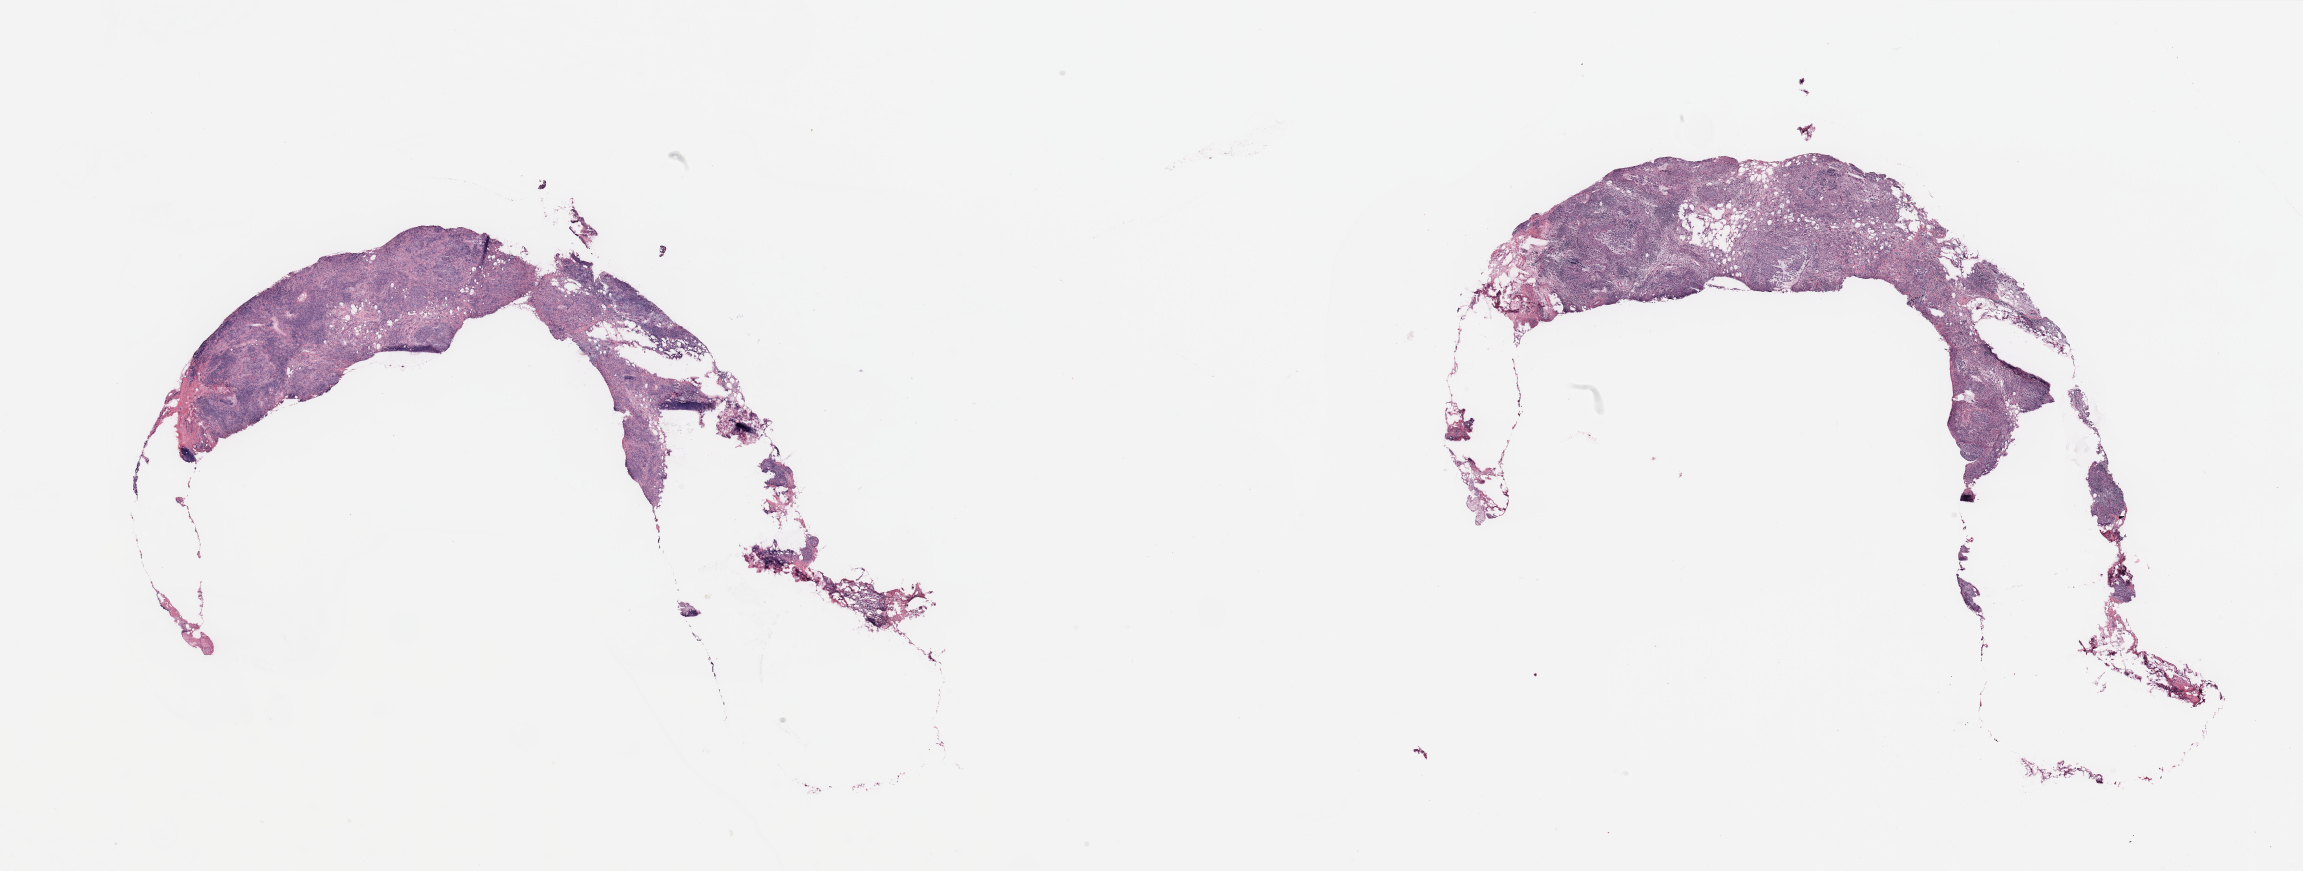
H&E whole-slide image — whole scanned area (about 36.4 x 13.8 mm) shown as a low-resolution overview; breast, tissue type not recorded.
Patient diagnosis (cohort enrolment): breast cancer (breast).